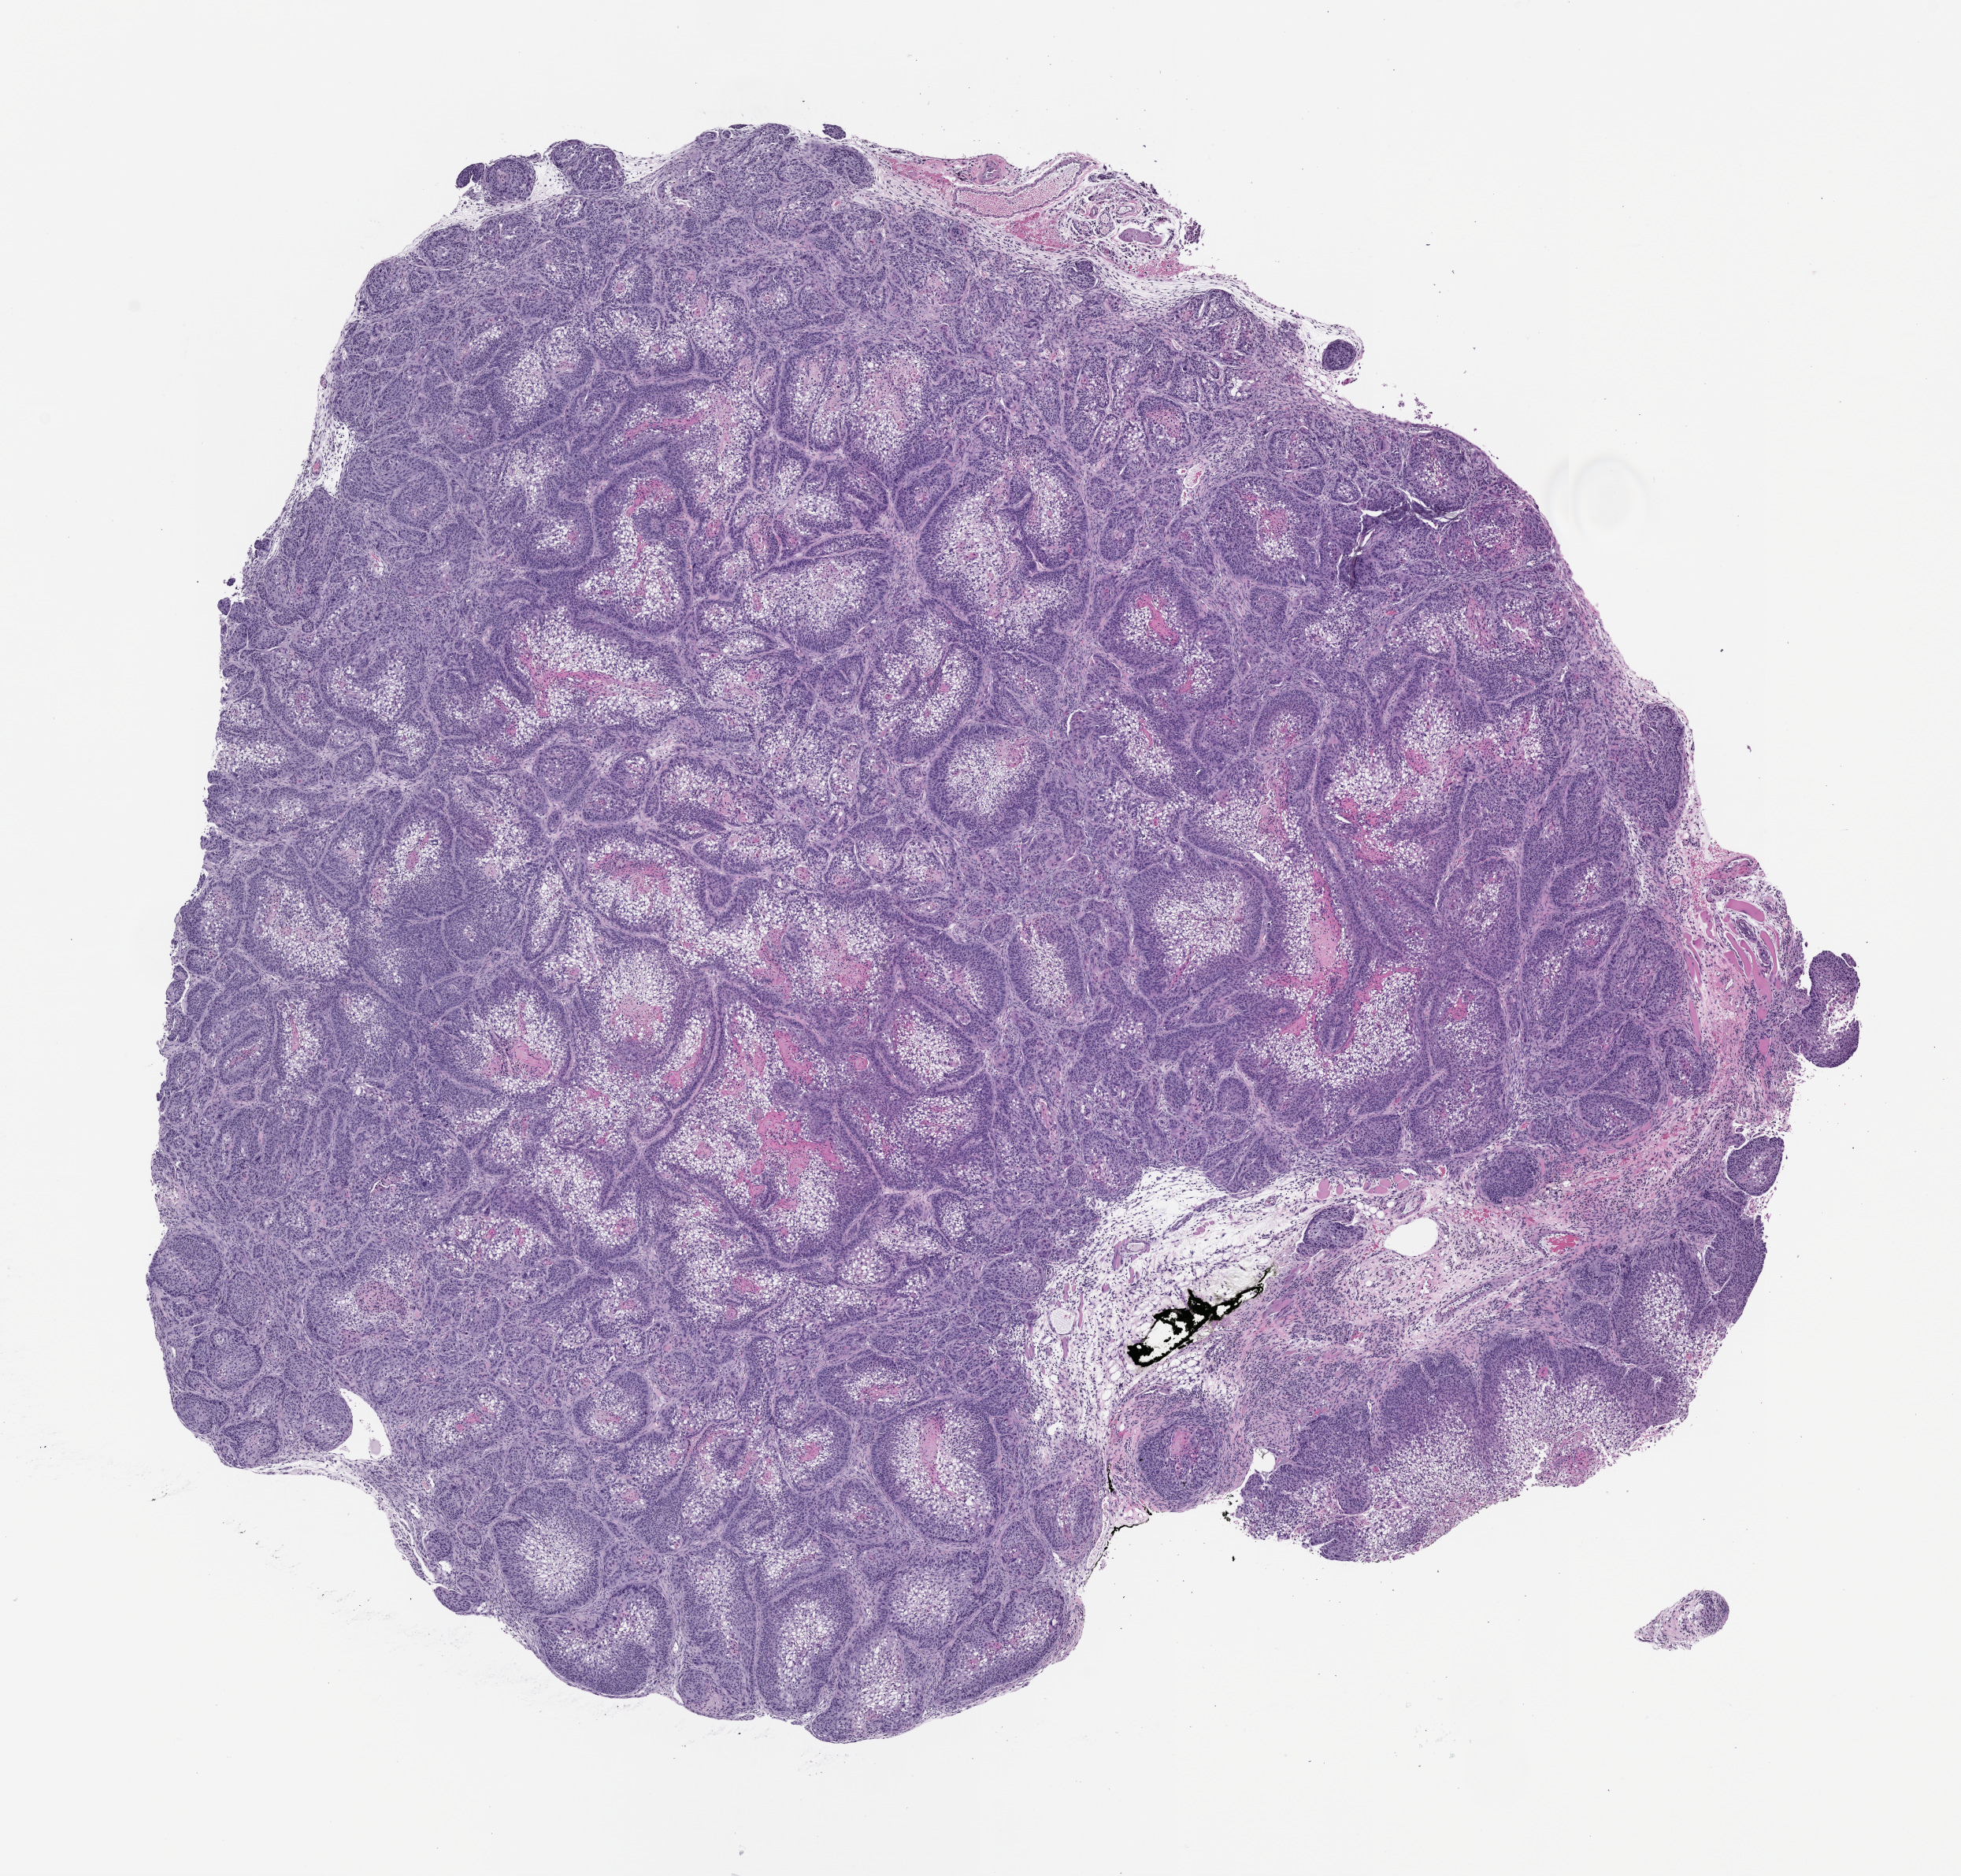
Haematoxylin and eosin whole-slide image of a patient-derived xenograft (PDX) tumor grown in a mouse, whole scanned area (about 10.0 x 9.6 mm) shown as a low-resolution overview. Formalin-fixed, paraffin-embedded (FFPE) tissue. Originating tumor site category: lung.
• originating patient diagnosis: Lung Squamous Cell Carcinoma